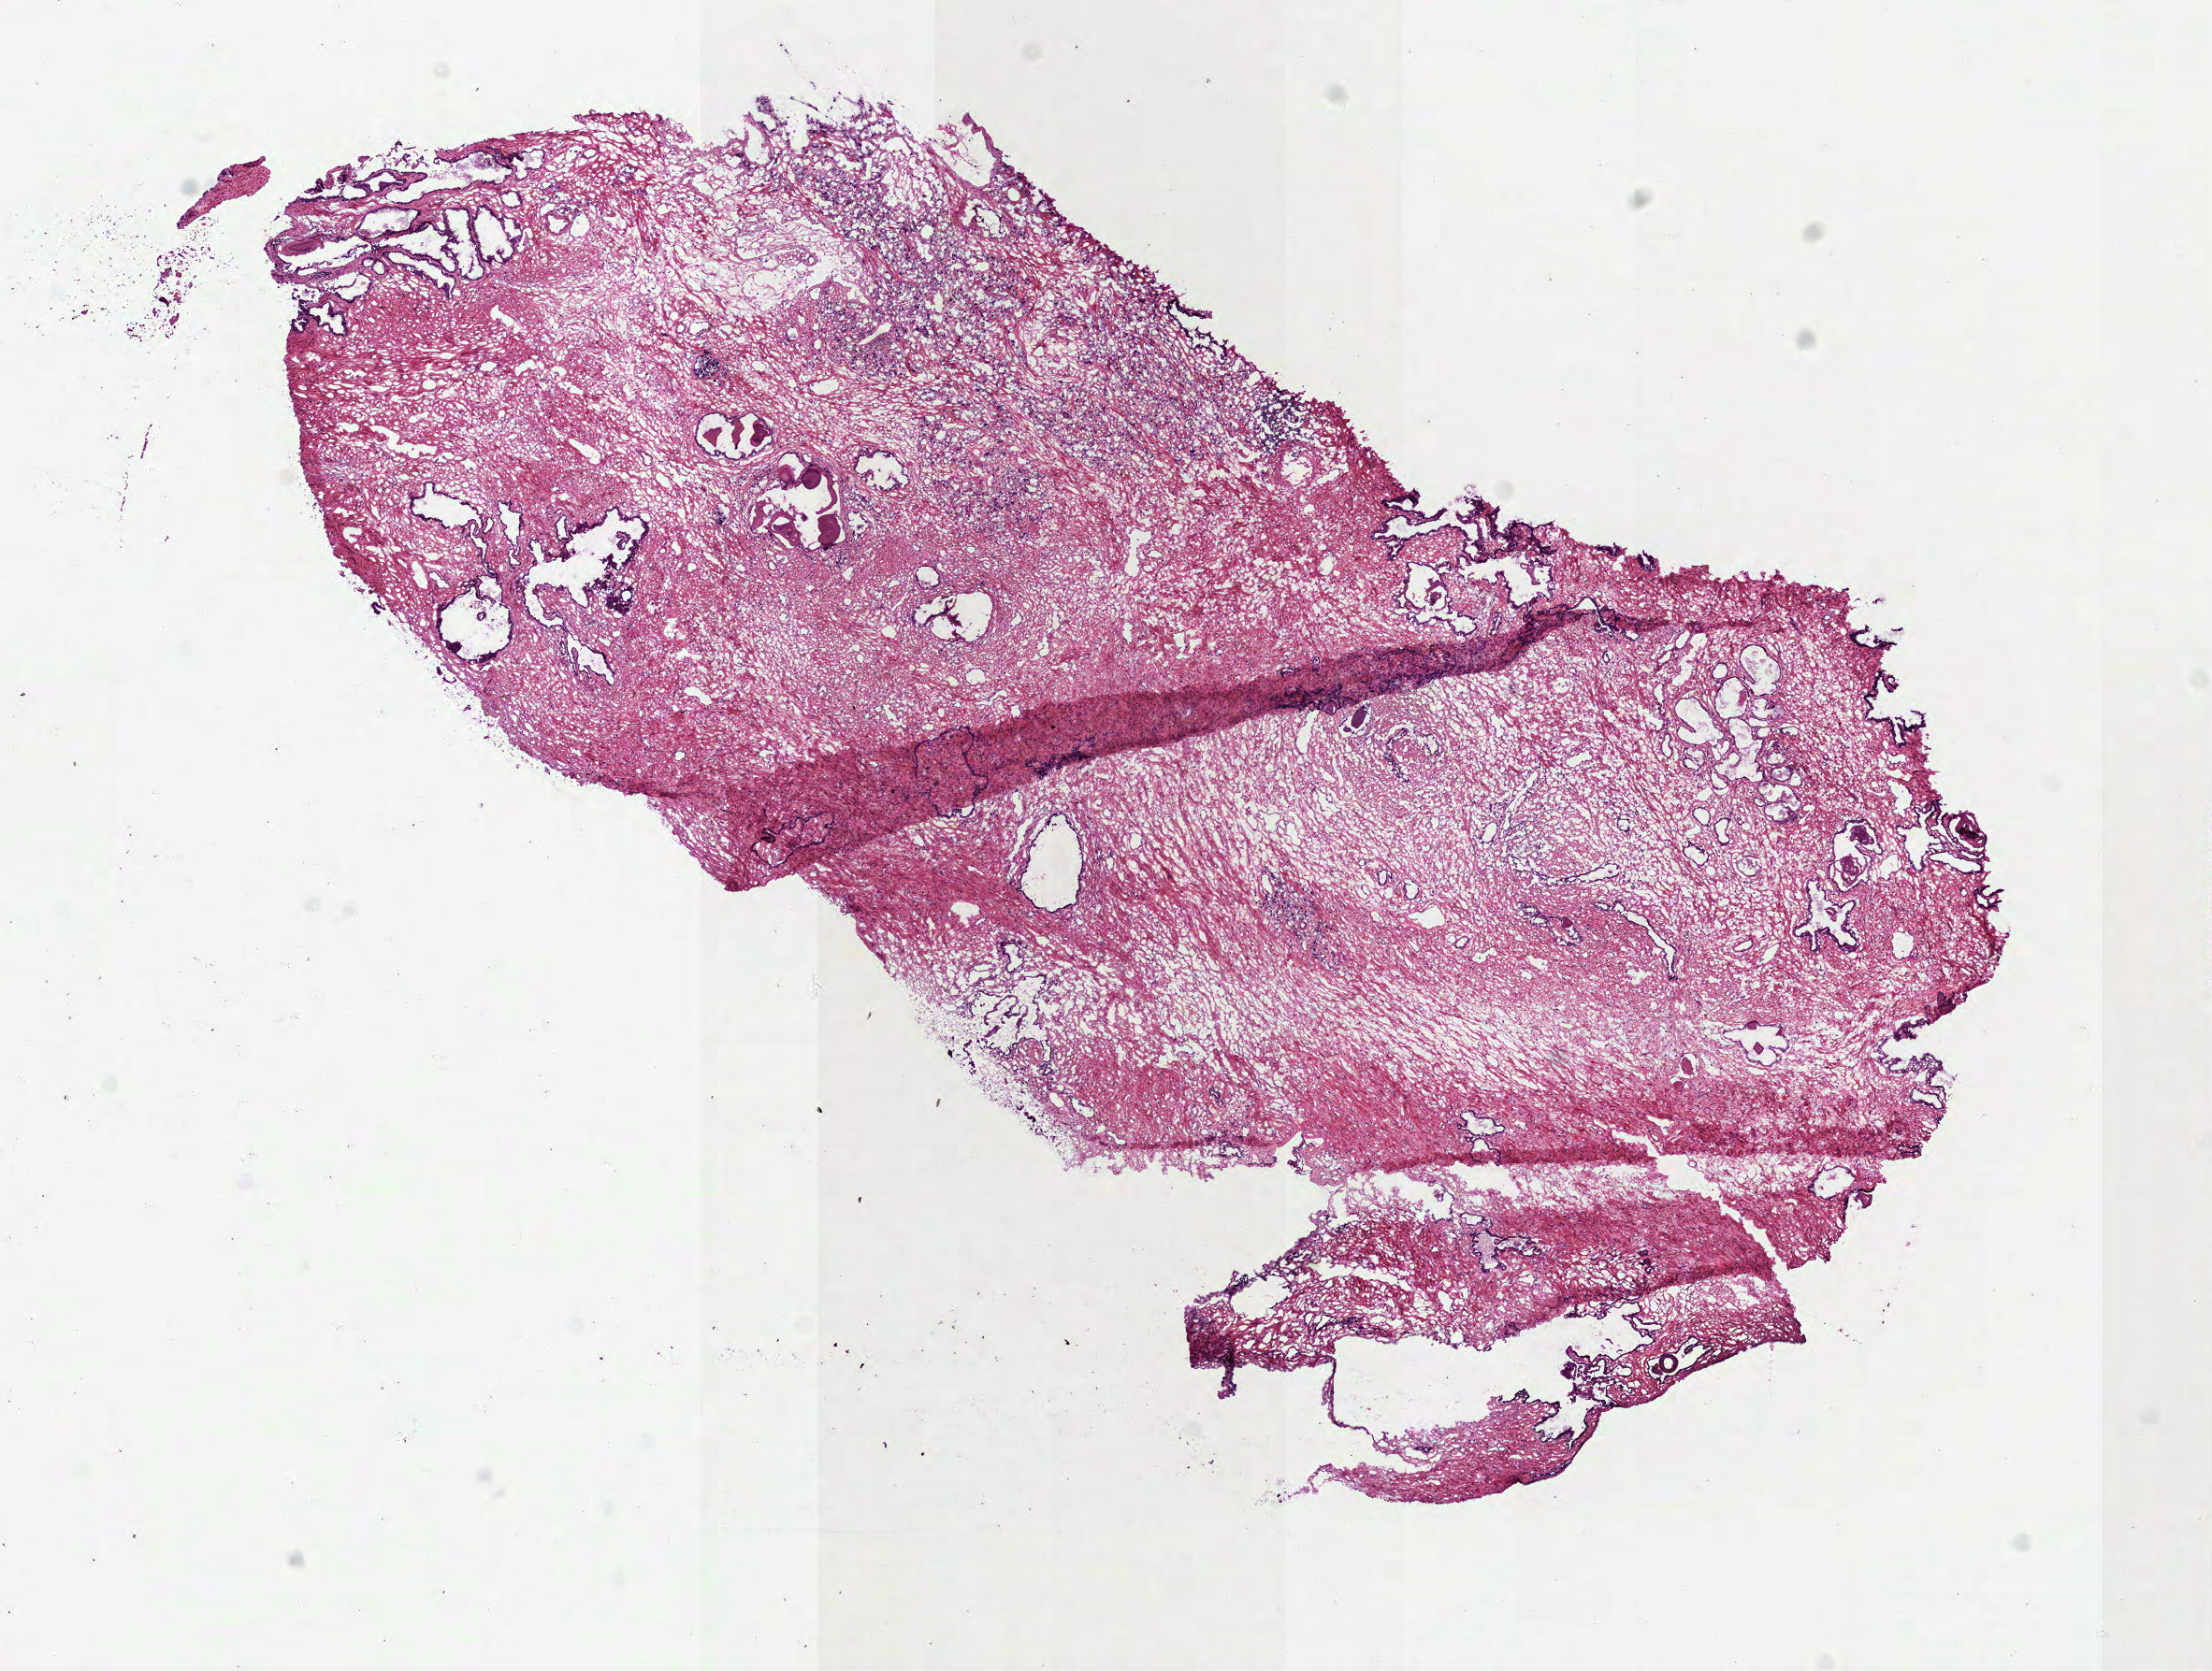
Whole-slide histology image, H&E — low-resolution overview of the scanned area, about 9.5 x 7.2 mm (from a 40x scan); frozen section; sample: primary tumour, prostate. Male patient; age at initial diagnosis 66 years. Gleason score: 9 (4+5). Pathologist review of this section (percent, as recorded): tumour cells 45%, tumour nuclei 45%, normal cells 15%, stromal cells 40%, necrosis 0%. Infiltration values recorded for this section: lymphocyte infiltration 5%, monocyte infiltration 0%, neutrophil infiltration 0%.
Diagnosis: Acinar cell carcinoma (prostate gland). Lymph nodes positive (case pathology): 0 of 13 examined.